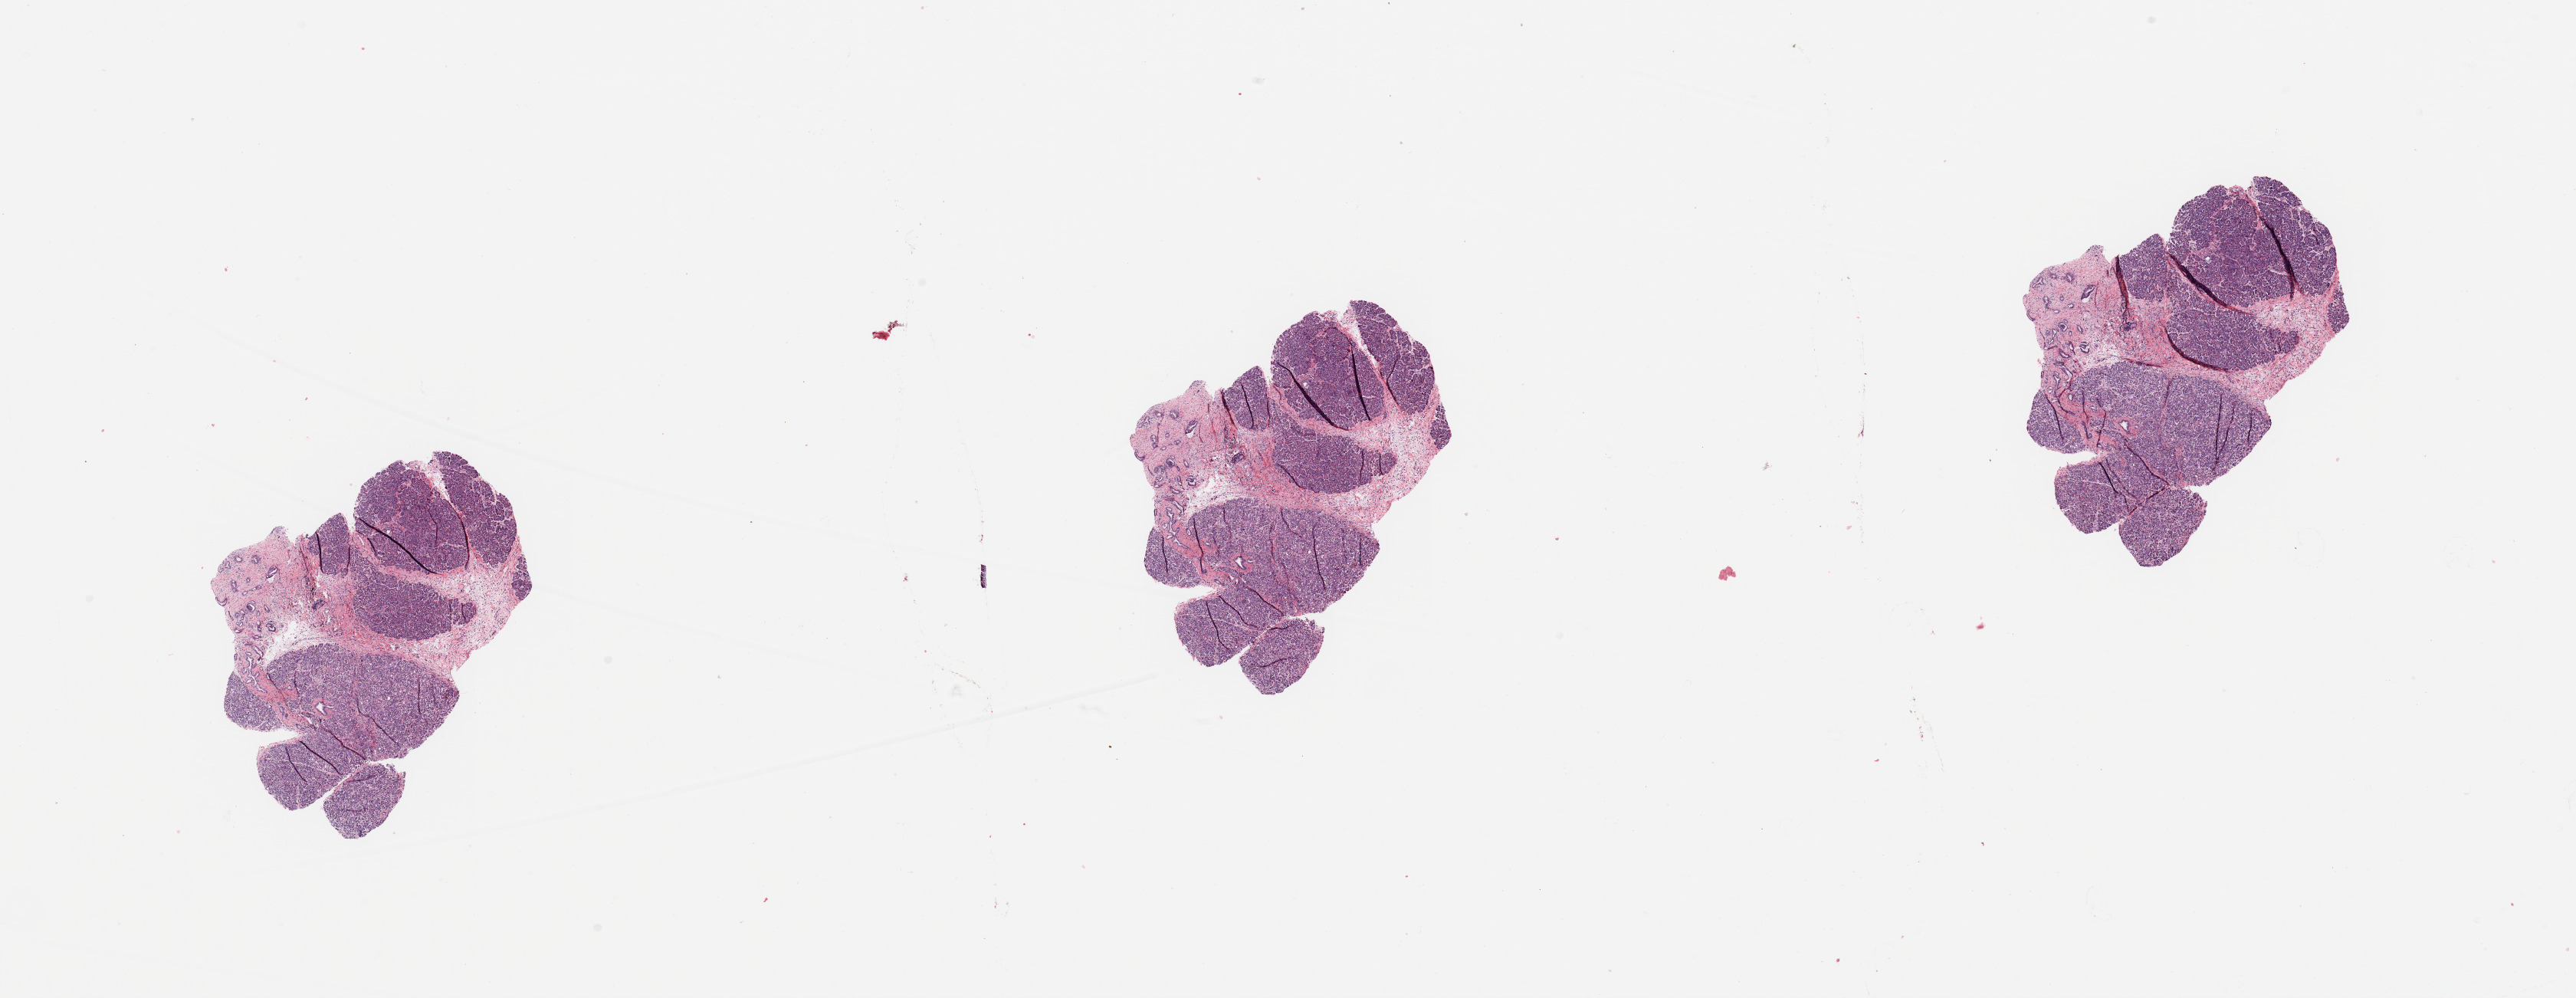
Hematoxylin and eosin (H&E) stained whole-slide image, a low-resolution overview of the entire scanned area, about 26.6 x 10.3 mm; normal (non-tumour) tissue sample, sampled site: pancreas. 34-year-old female patient.
This section: normal (non-tumour) tissue from the same patient. Patient diagnosis: Infiltrating duct carcinoma, NOS.